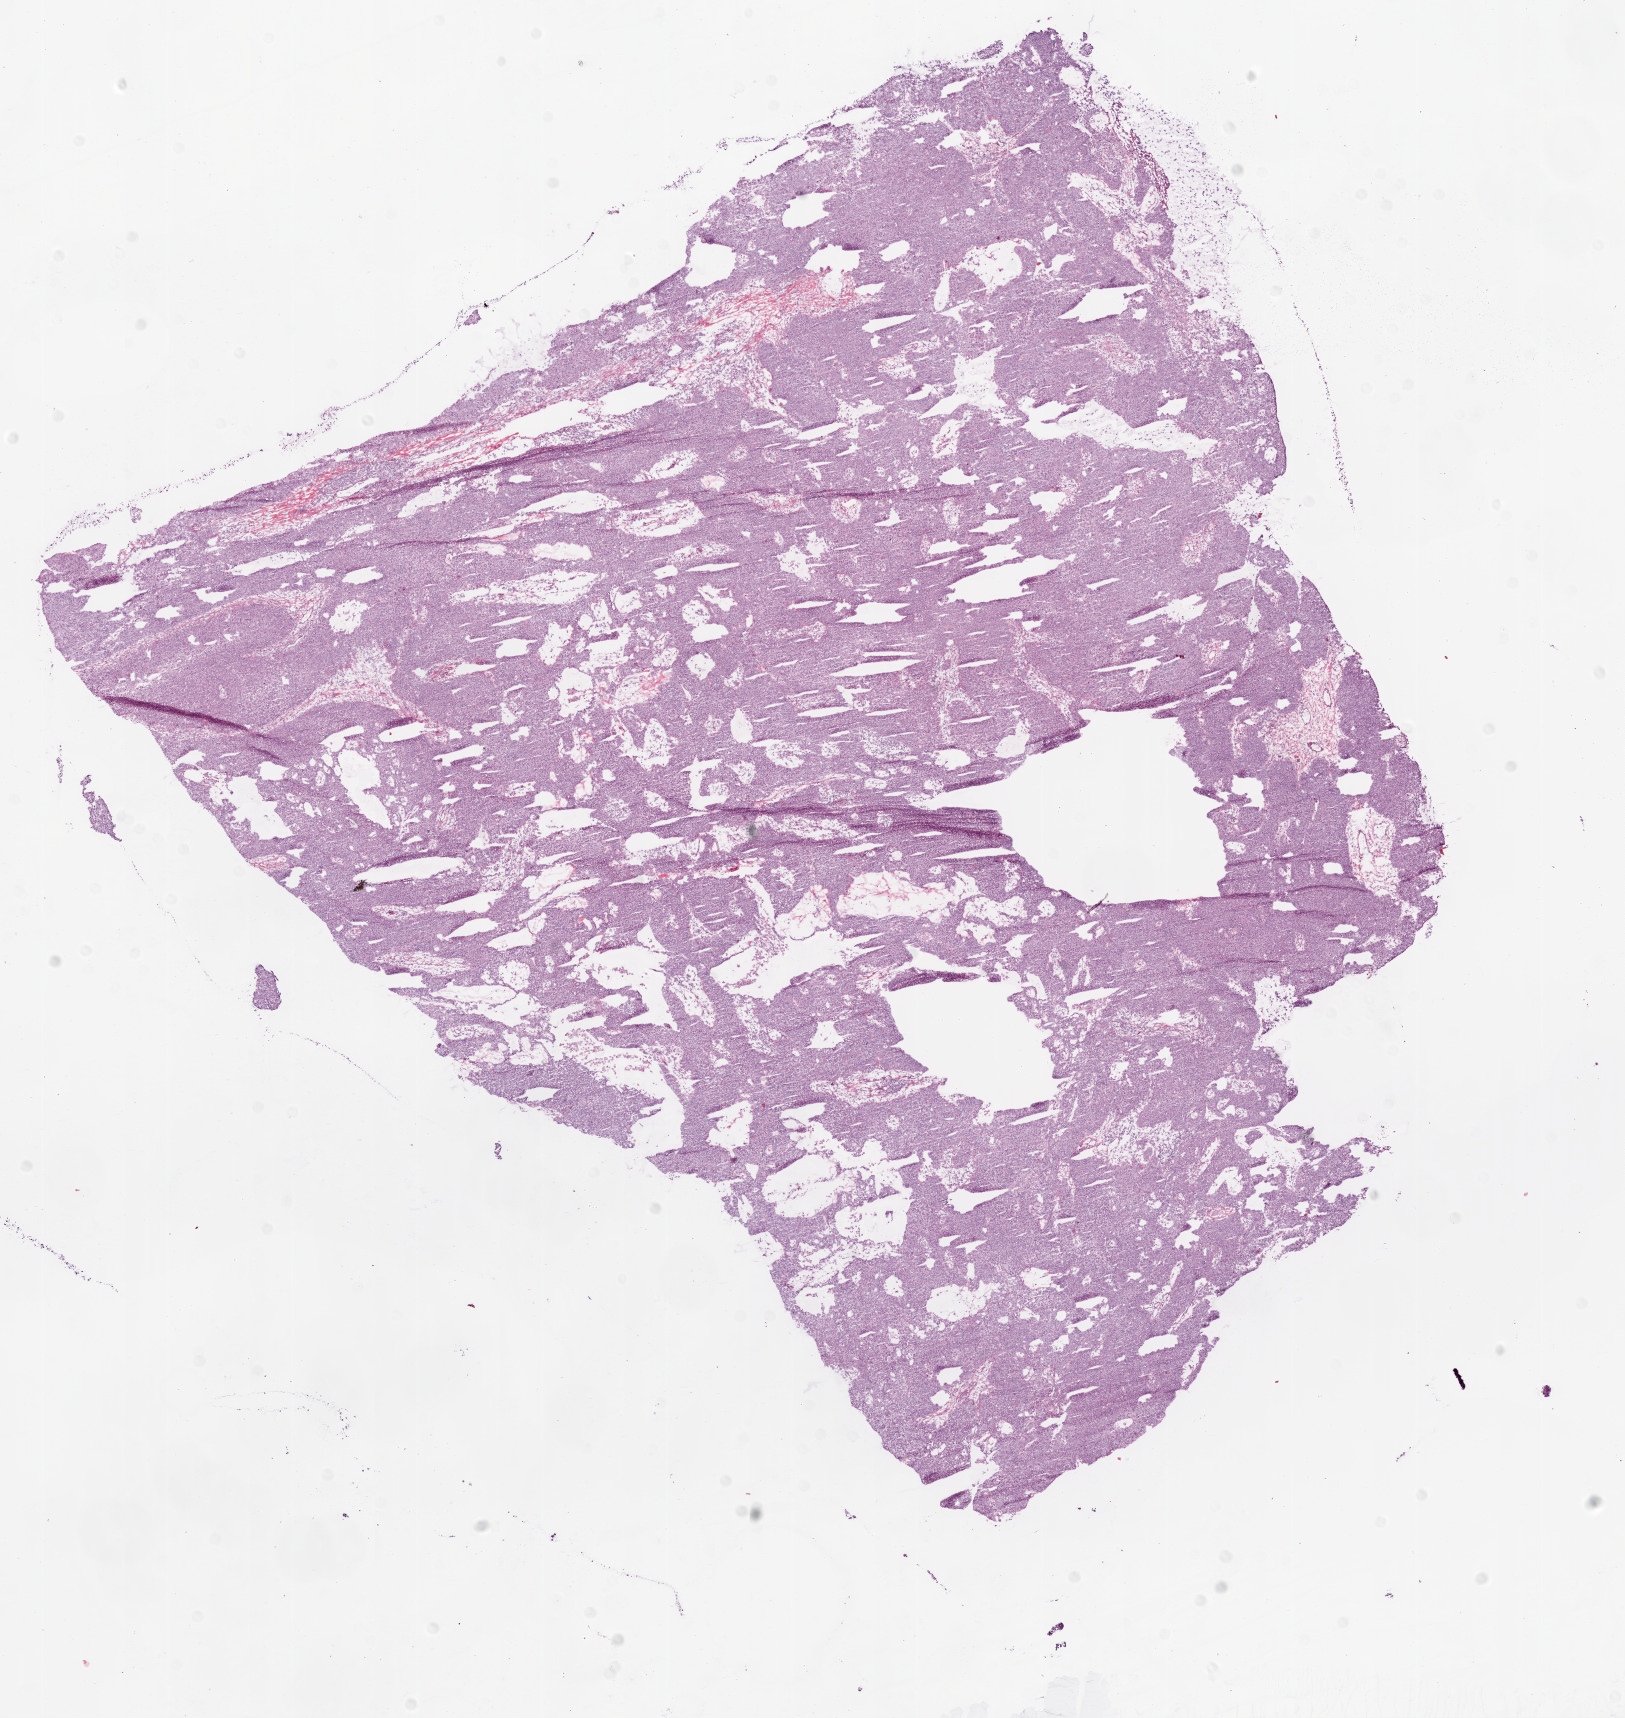
Digitized Hematoxylin and eosin (H&E) stained tissue section (whole slide), a low-resolution overview of the entire scanned area, about 13.0 x 13.8 mm (slide scanned at 20x); frozen section from the bottom of the tissue portion; sample: primary tumour, ovary. Female patient; age at initial diagnosis 50 years. Histologic grade: G3 (poorly differentiated). Pathologist review of this section (percent, as recorded): tumour cells 94%, tumour nuclei 95%, normal cells 0%, stromal cells 5%, necrosis 1%.
• FIGO stage: IIC
• laterality: bilateral
• histologic diagnosis: Serous cystadenocarcinoma, NOS